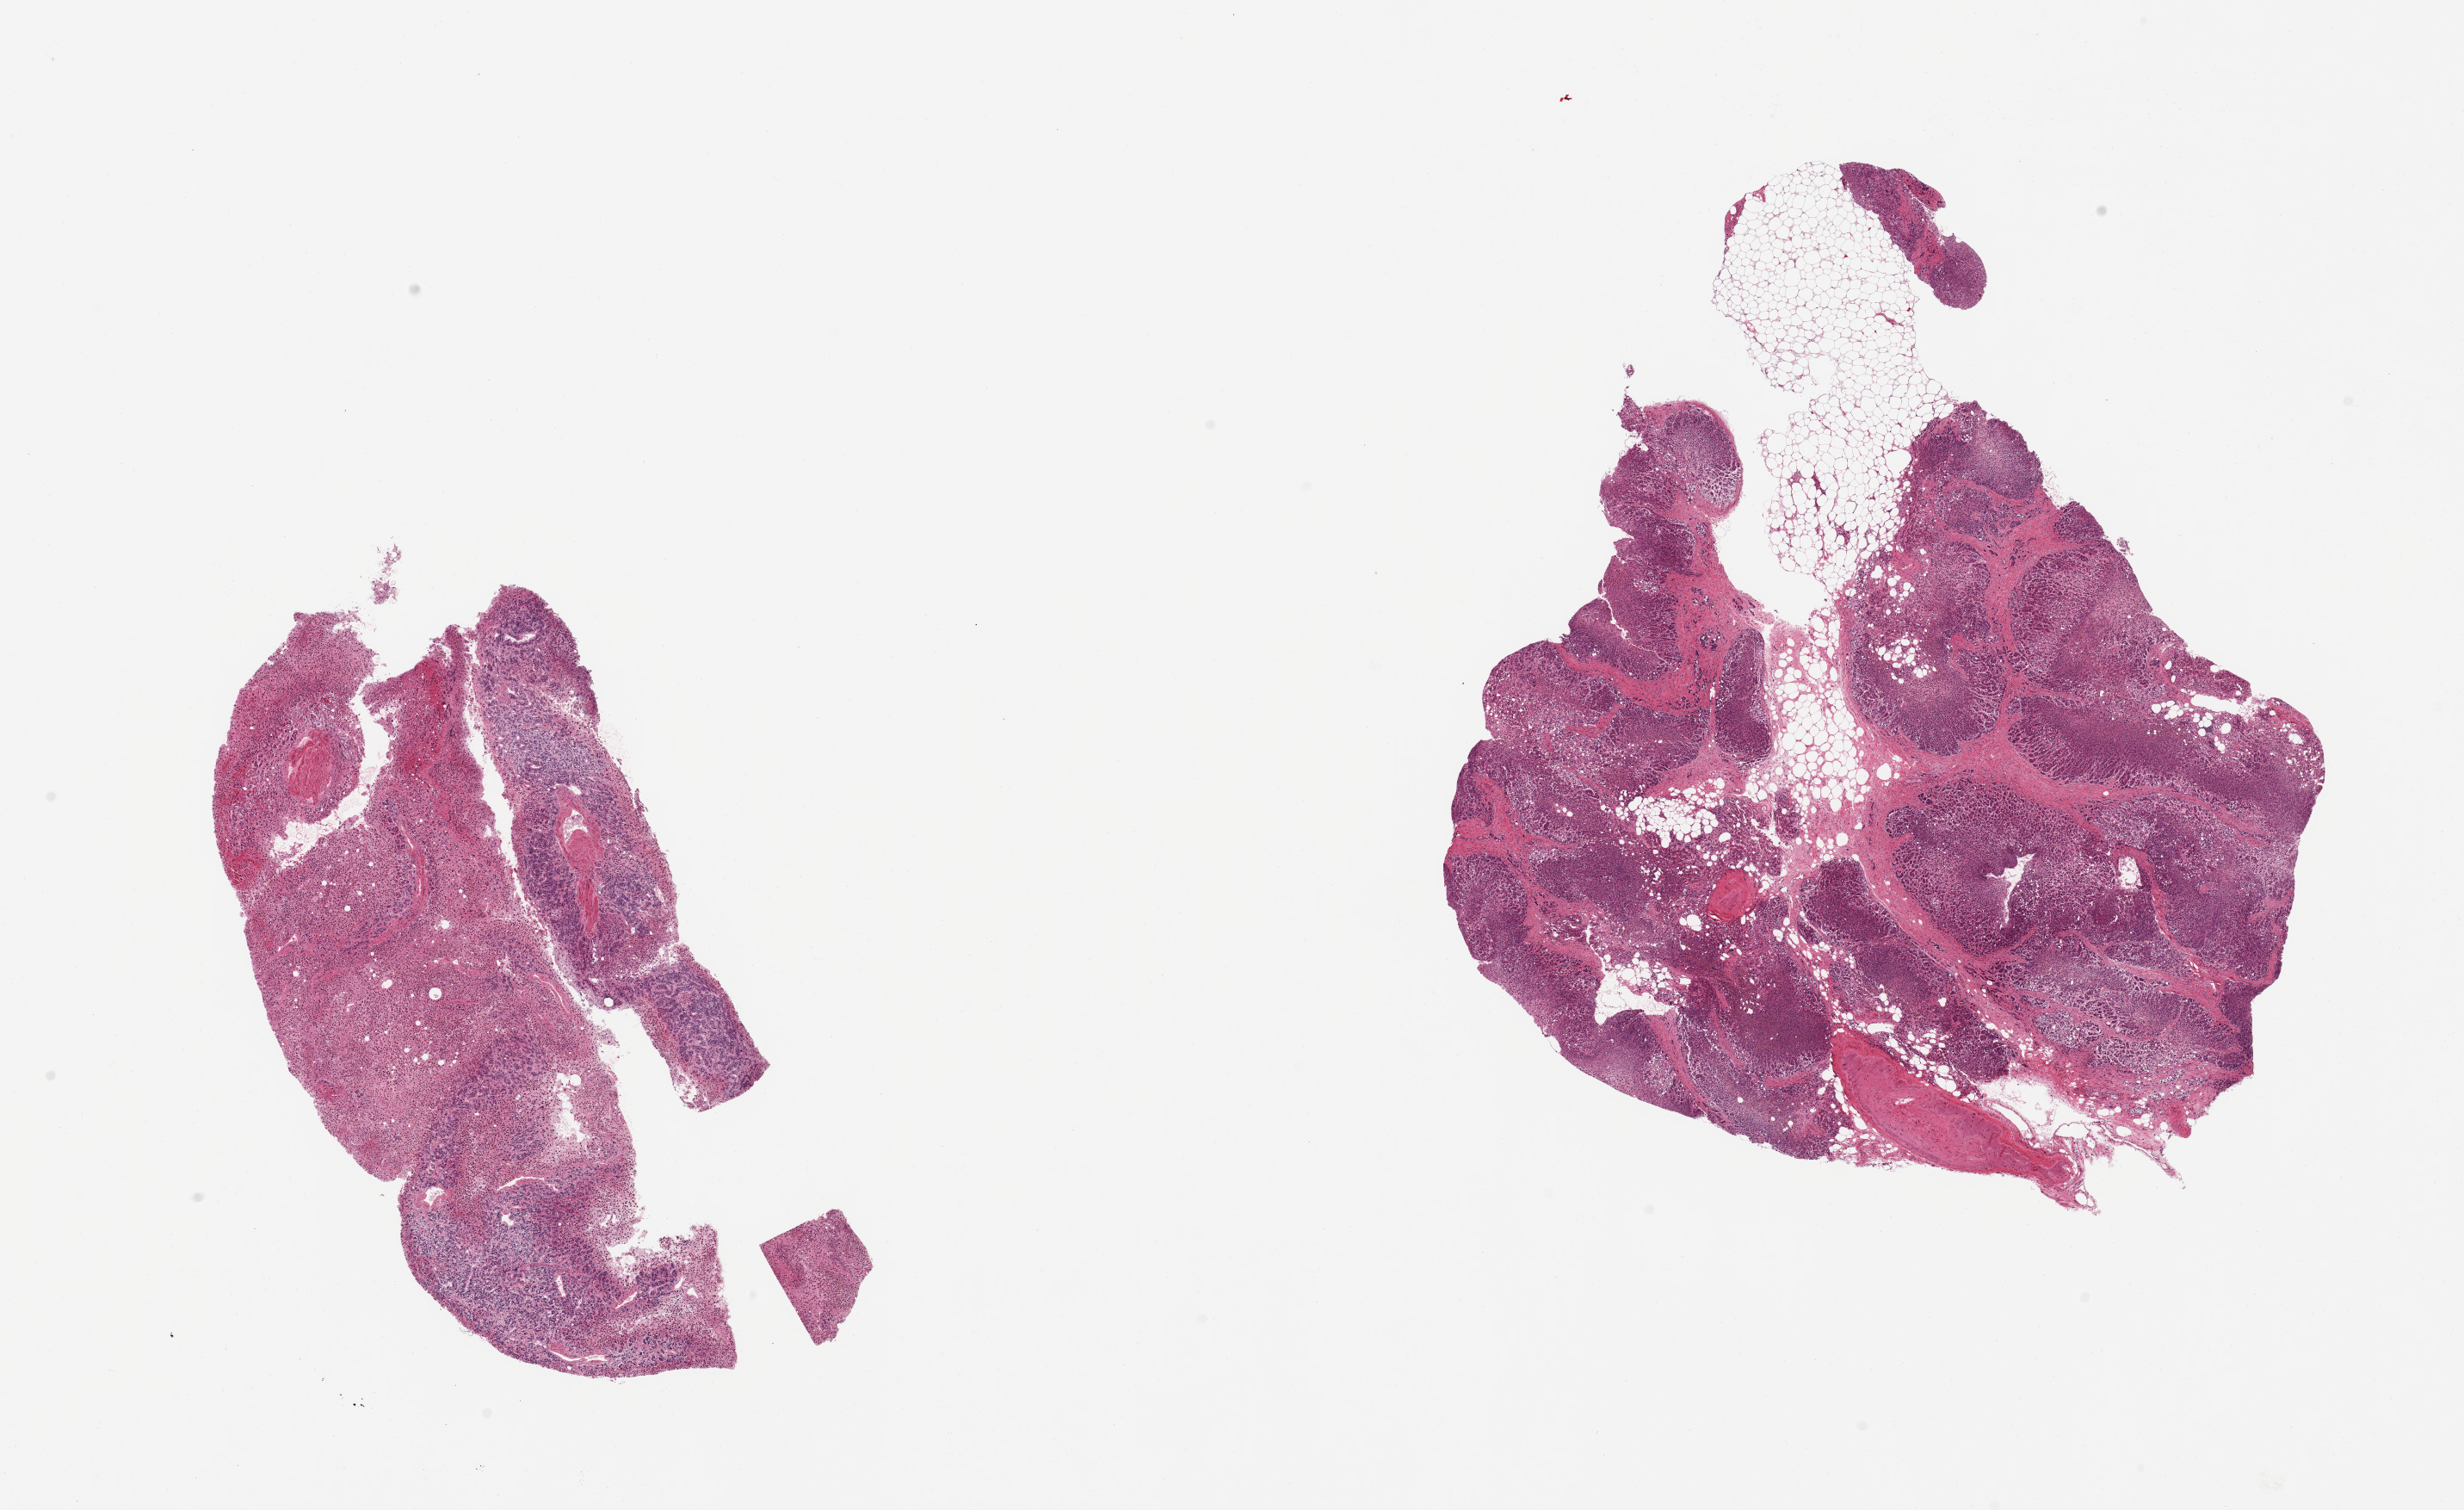
Digitized H&E-stained section, a low-resolution overview of the entire scanned area, about 22.6 x 13.9 mm (slide scanned at 20x); PAXgene-fixed, paraffin-embedded tissue; target tissue: adrenal gland; tissue donor sample. Donor: male.
Review note (as recorded): 2 pieces, cortex, markedly autolyzed, ~15-20% adherent fat.